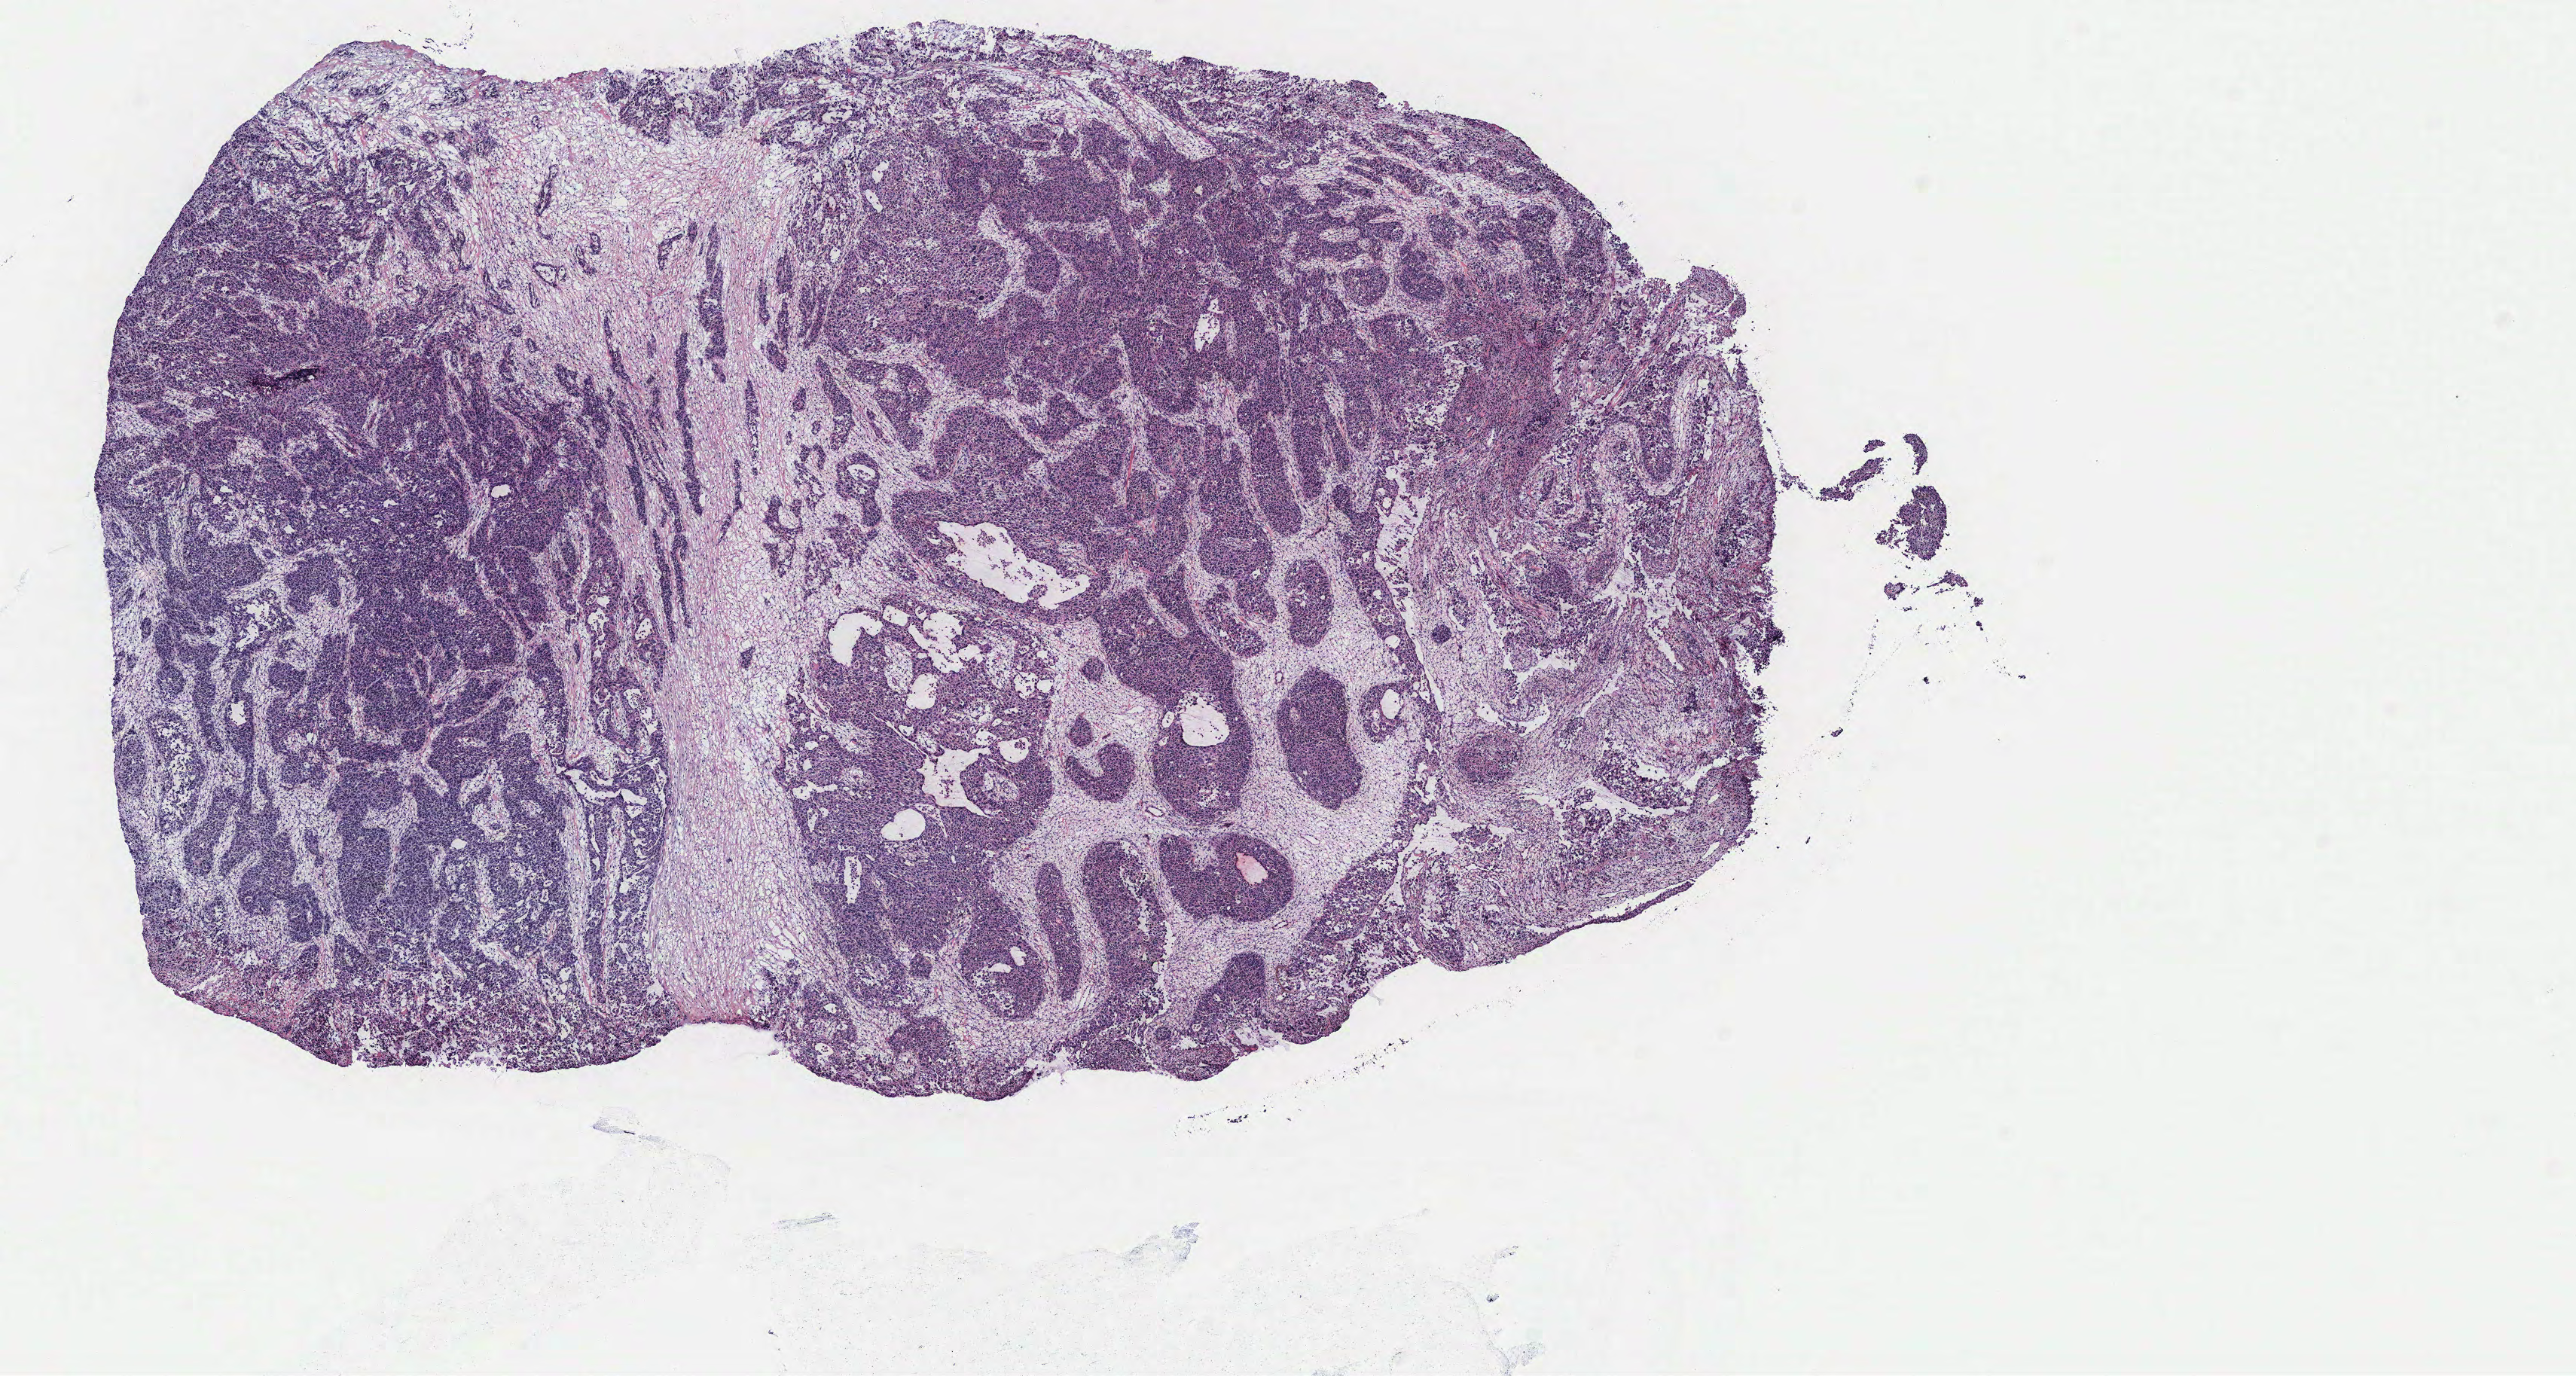
Hematoxylin and eosin (H&E) stained whole-slide image, whole scanned area (about 13.7 x 7.3 mm, slide scanned at 40x) shown as a low-resolution overview, tumour tissue sample, ovary. Patient: female, age 50 years.
* primary tumour site (as recorded): ovary
* diagnosis: Serous adenocarcinoma, NOS